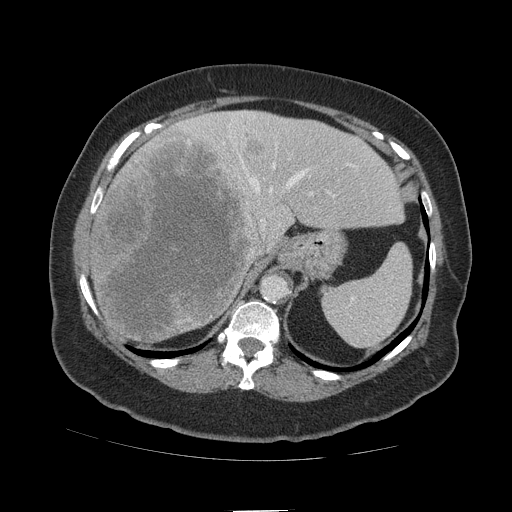
Contrast-enhanced abdominal CT (liver protocol), one axial slice; slice 79 of 109 in the series (ordered by position); soft-tissue window (W 400 / L 40 HU); 2.5 mm slice thickness; 512 × 512 image matrix. From the clinical record (not read from this slice): diagnosis: hepatocellular carcinoma (patient treated with transarterial chemoembolisation; whether this scan precedes or follows treatment is not stated here); TNM stage (as recorded): Stage-IVB; Child-Pugh class: A; tumour differentiation: poorly differentiated.
Structures marked on this image (semi-automatic segmentation, software-assisted and operator-edited):
- liver parenchyma outside the tumour (the mass and vessels are separate outlines, so this box may not span the whole liver): bounding box (x1, y1, x2, y2) in pixels: (84, 110, 404, 340)
- mass: (91, 128, 271, 343)
- liver vessels: (96, 112, 355, 207)